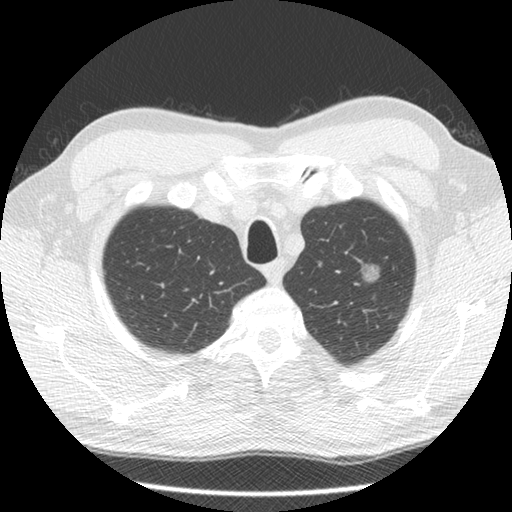
Low-dose screening chest CT, one axial slice; position 116 of 132 along the scan axis; lung window (W 1500 / L -600 HU); 512 × 512 image matrix, field of view 340 × 340 mm.
Annotated regions visible in this slice (manually delineated by an expert):
- lesion 1 (tumor, upper lobe of left lung): bounding box (x1, y1, x2, y2) in pixels: (354, 262, 379, 285)